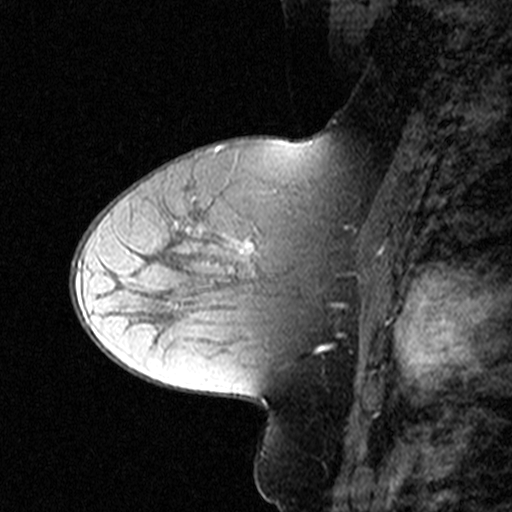
Breast MRI (dynamic contrast-enhanced), one sagittal slice; slice 24 of 44 in the series (ordered by position); dynamic contrast-enhanced study with each time point stored as its own series, time point 2 of 3 at this slice position (early post-contrast, ordered by acquisition time); 1.5 T; TE 4.5 ms, TR 11 ms; 3 mm slice thickness; 512 × 512 image matrix, field of view 200 × 200 mm. Female patient, age 50 years. Case-level facts recorded for this patient, not image findings: setting: breast cancer imaged before/during neoadjuvant chemotherapy; receptor status: HR-positive, HER2-negative.
Outlined on this slice (semi-automatic segmentation, software-assisted and operator-edited):
- analysis volume of interest (the breast-tissue region the enhancement analysis was run in; not a lesion): bounding box [x1, y1, x2, y2] px = [180, 198, 349, 311]
- tumour enhancement mask (voxels above the 90 % enhancement threshold inside the analysis volume of interest): [232, 241, 346, 308]